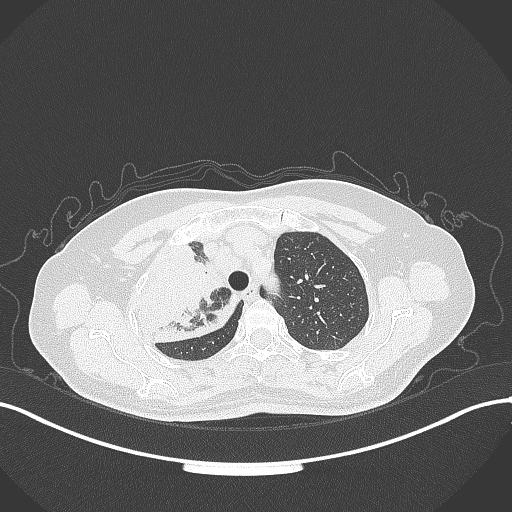
Chest CT, one axial slice. Lung window (W 1500 / L -600 HU). 1 mm slice thickness. 512 × 512 image matrix. Female patient, age 60 years. From the clinical record (not read from this slice): clinical TNM (as recorded): T3 N1 M1.
Outlined on this slice (bounding box drawn by a radiologist):
- lung tumour (recorded histology: adenocarcinoma): box from (x=134, y=232) to (x=242, y=345) px